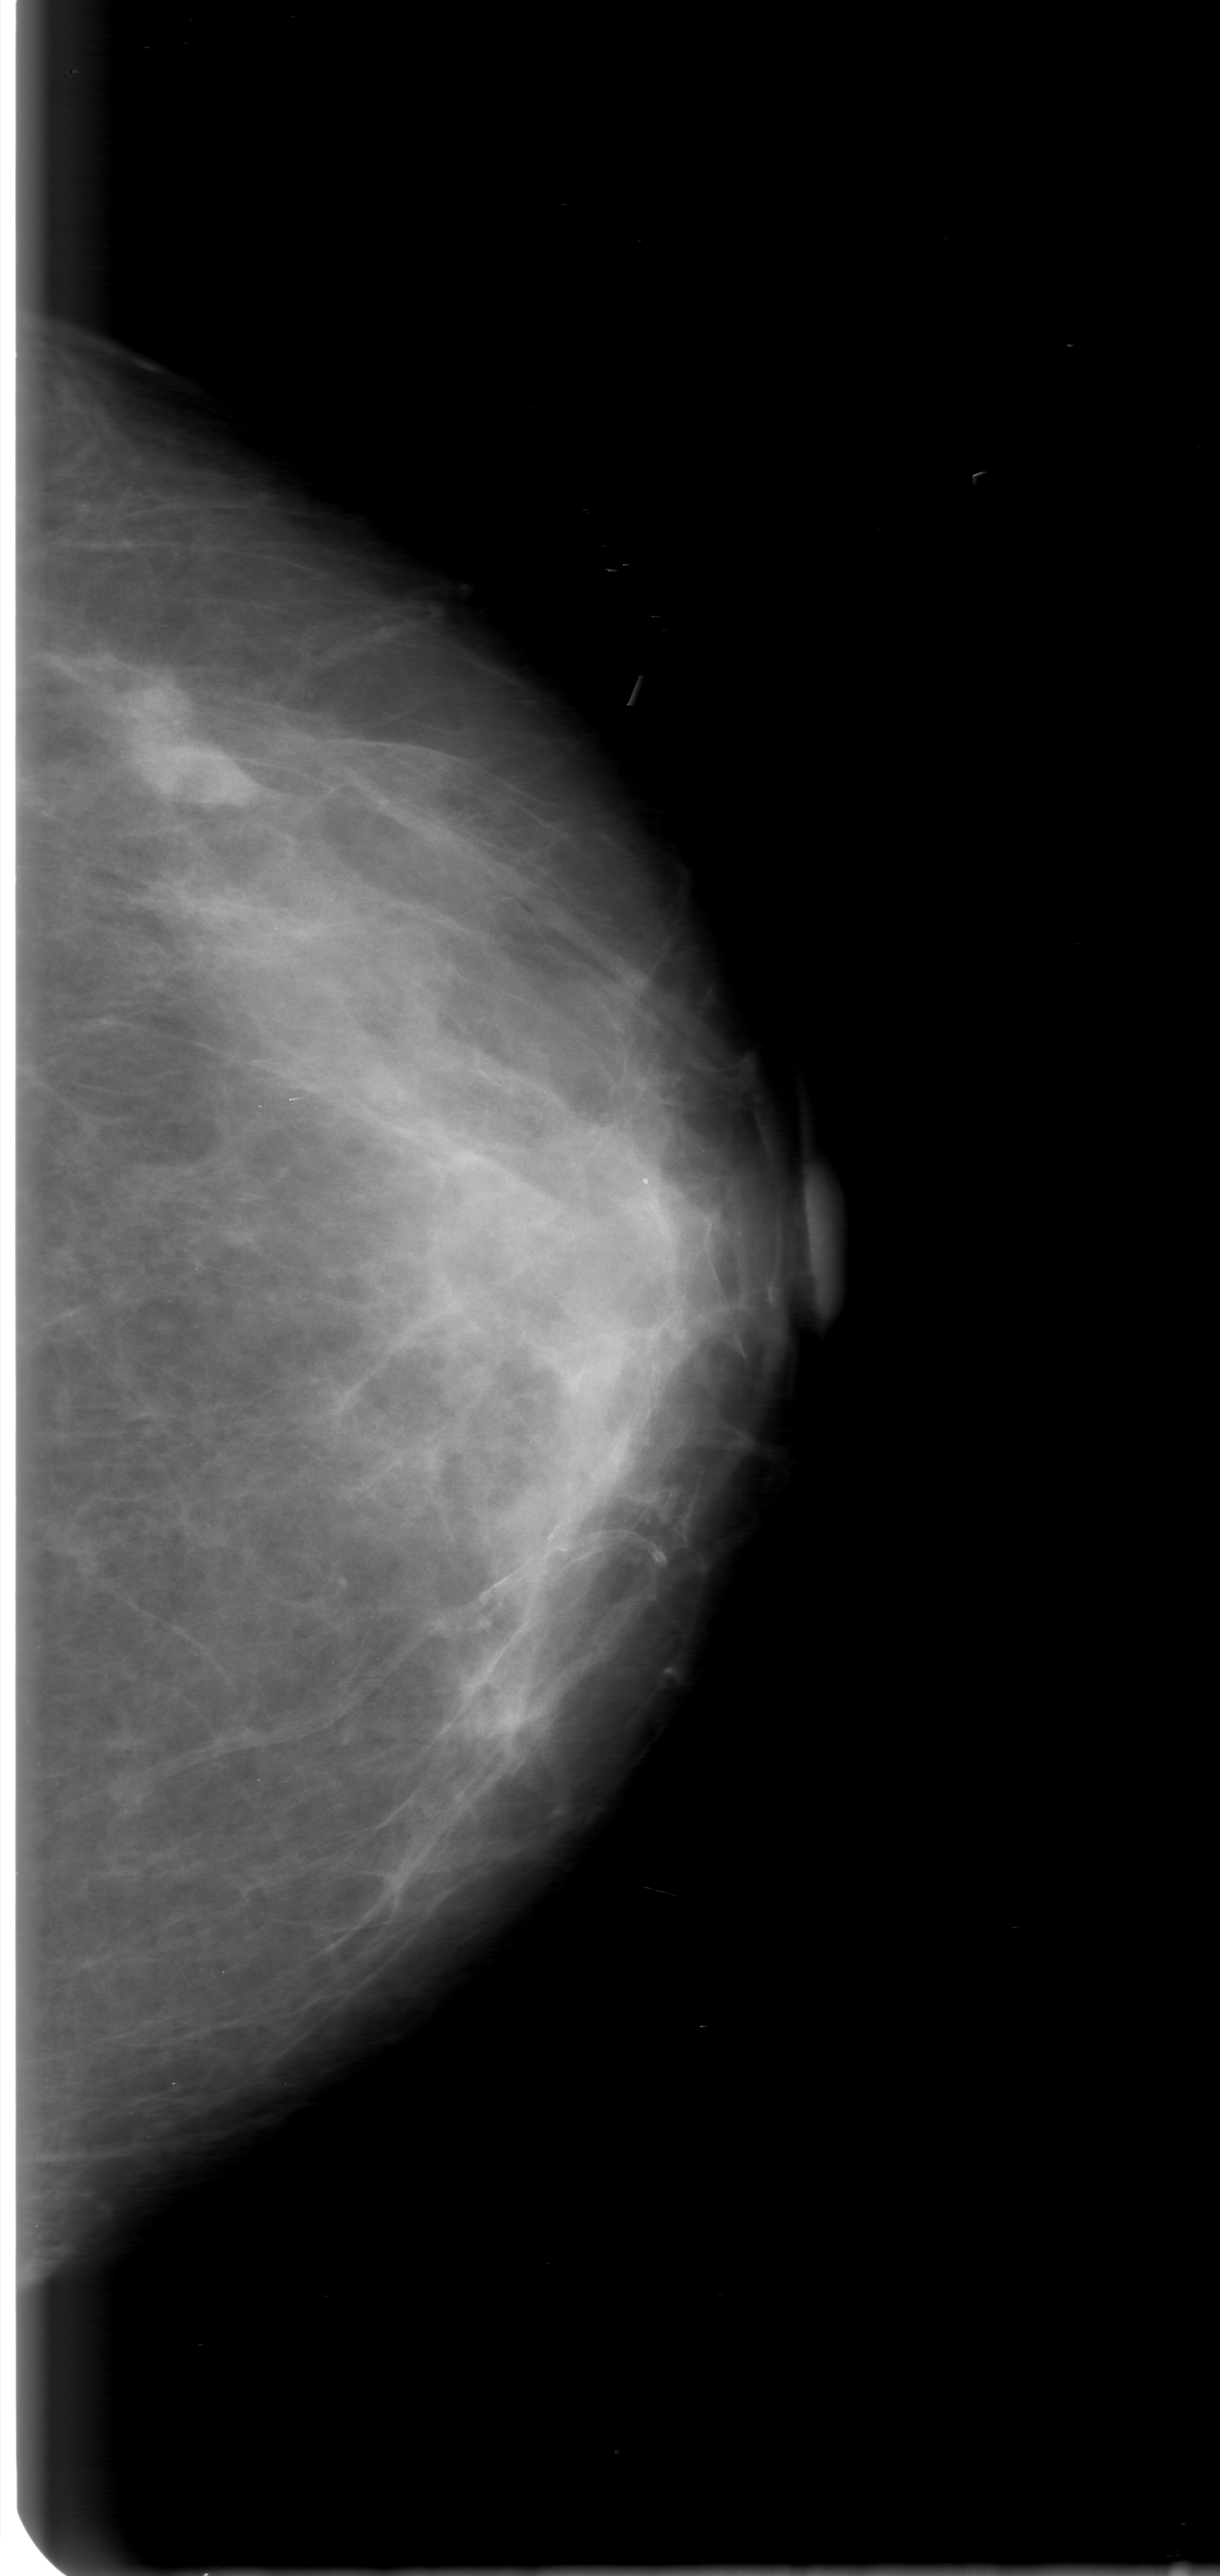
Digitized screen-film mammogram, left breast, CC view.
Finding: mass, shape lobulated, margins obscured; BI-RADS assessment category 0 (incomplete: needs additional imaging); pathology (as recorded): malignant.